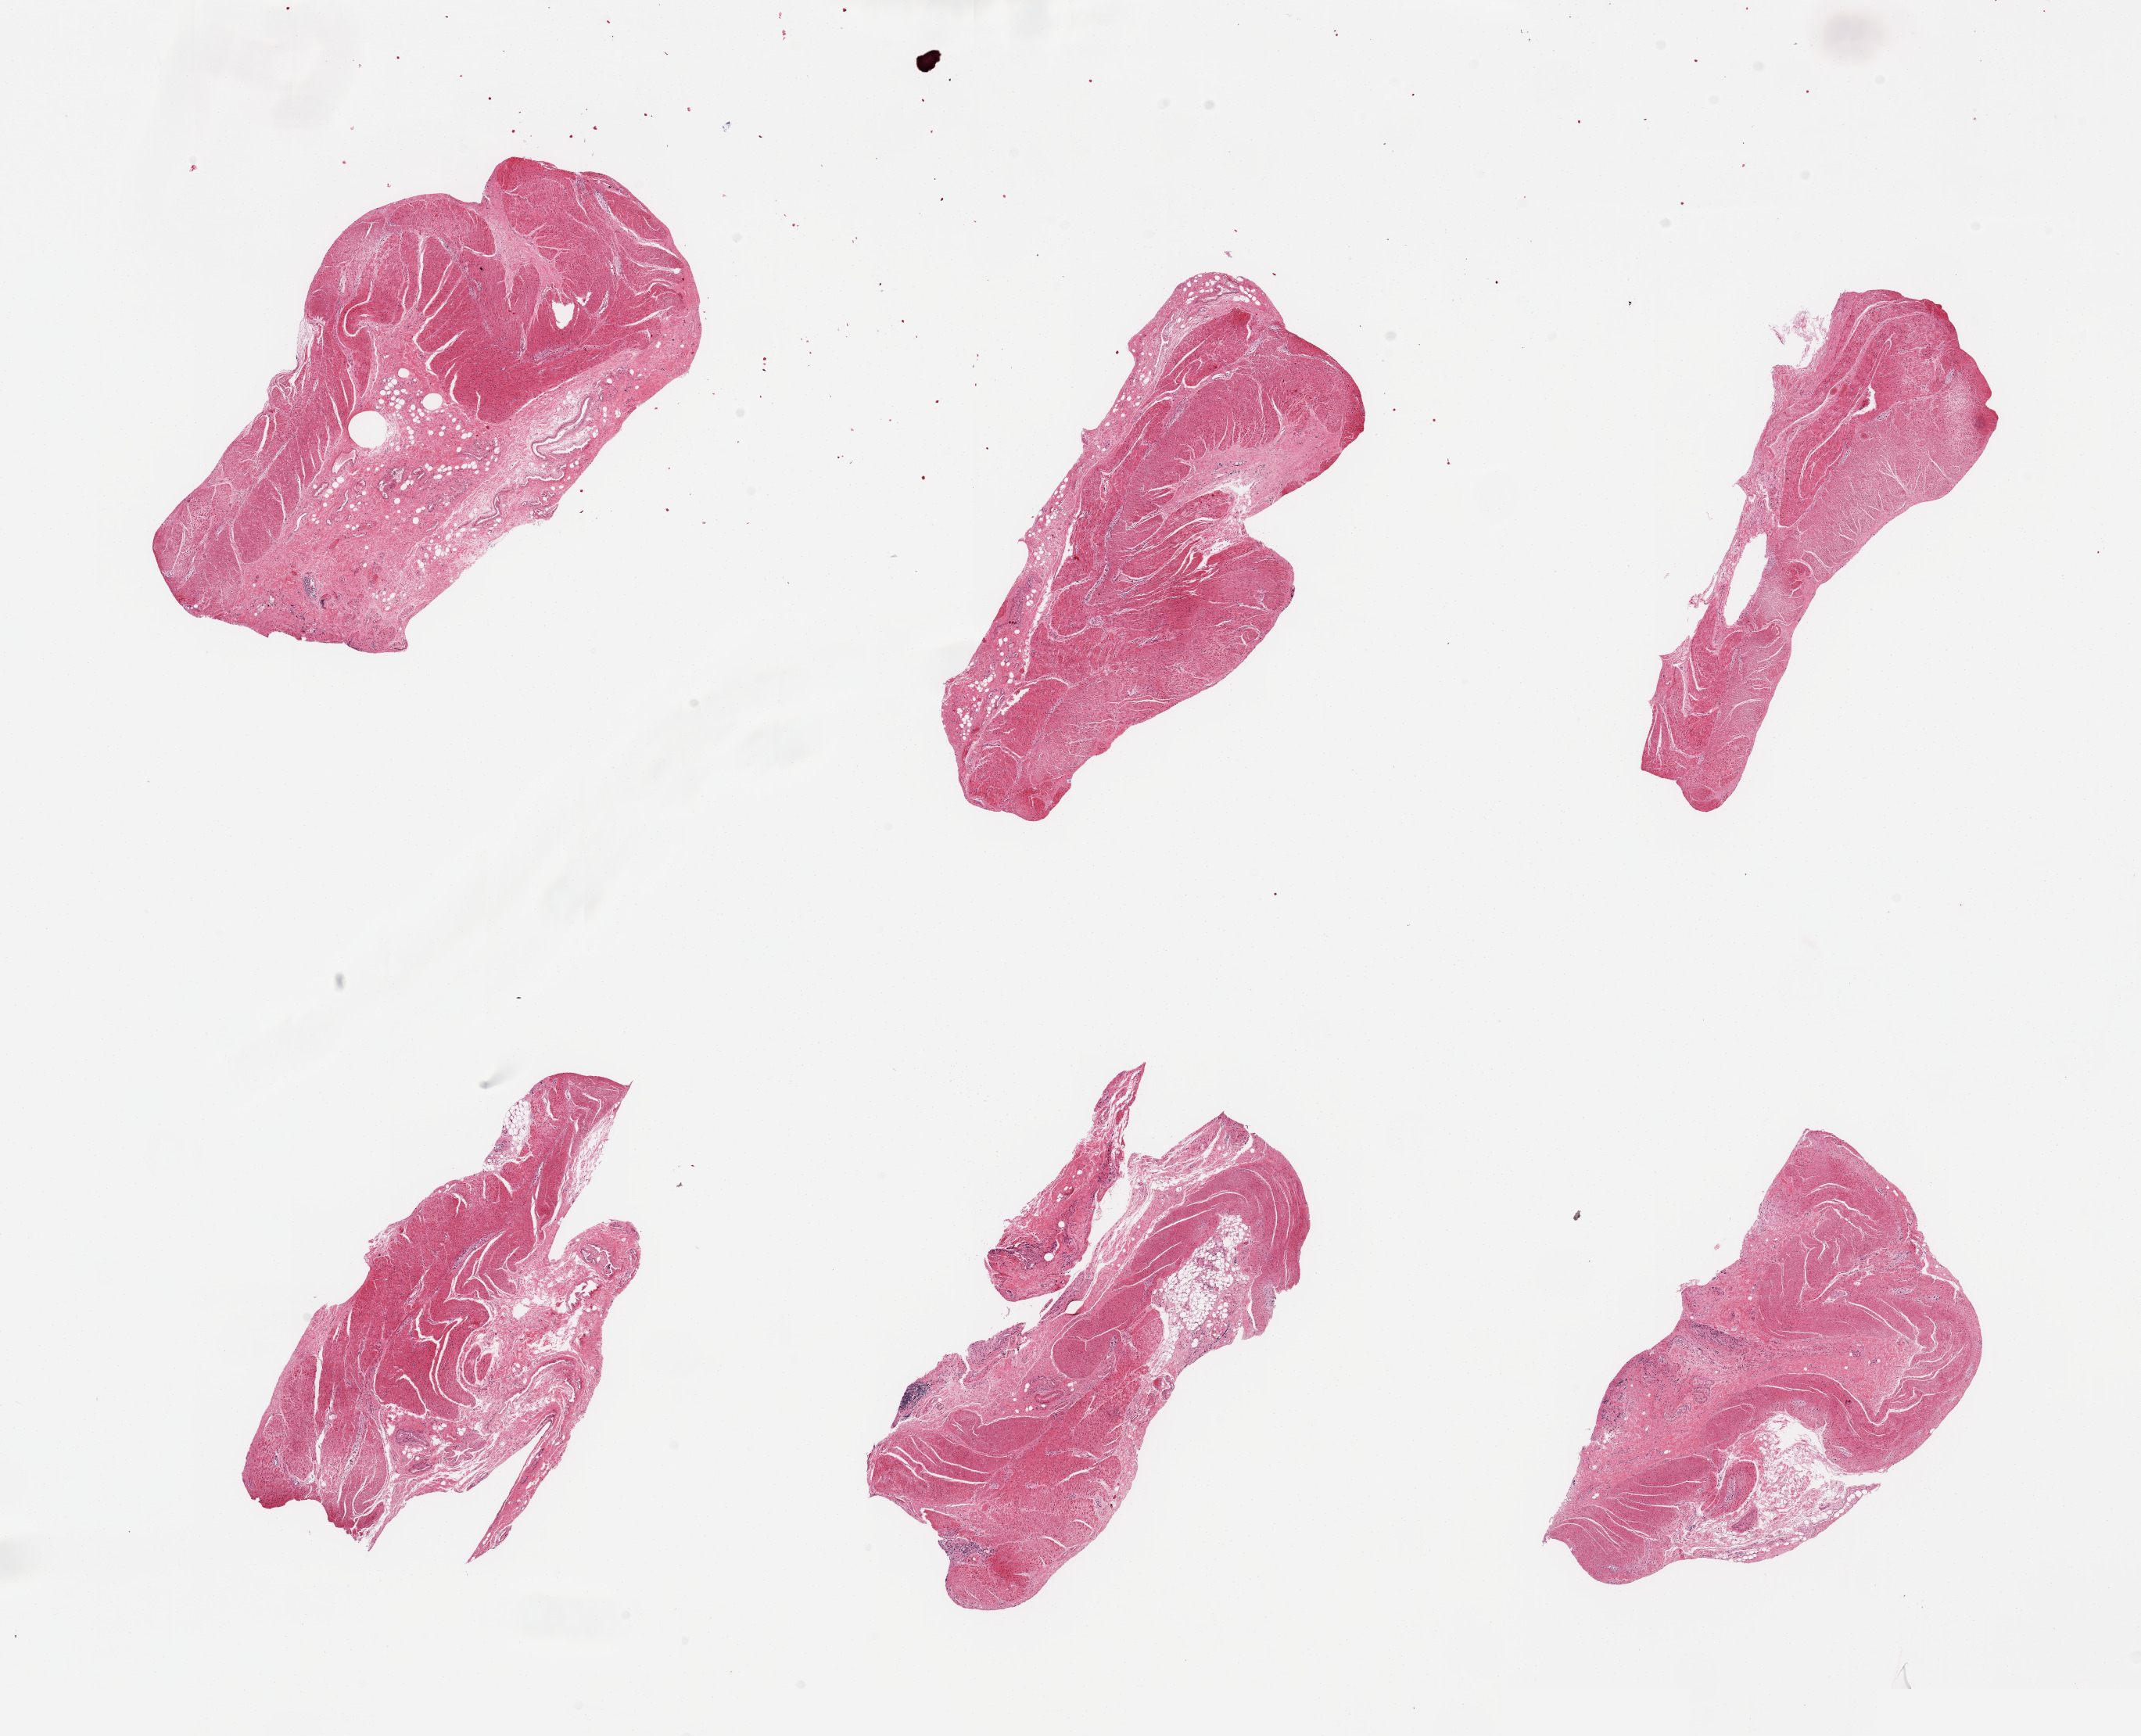
Whole-slide image, H&E stain — shown as a low-resolution overview of the whole scanned area (about 21.7 x 17.6 mm, acquisition: 20x scan). PAXgene-fixed, paraffin-embedded tissue. Sampled site (target tissue): sigmoid colon. Donor tissue sample. Female donor.
Reviewer comment on this tissue sample: 6 pieces, confirmed target muscularis.